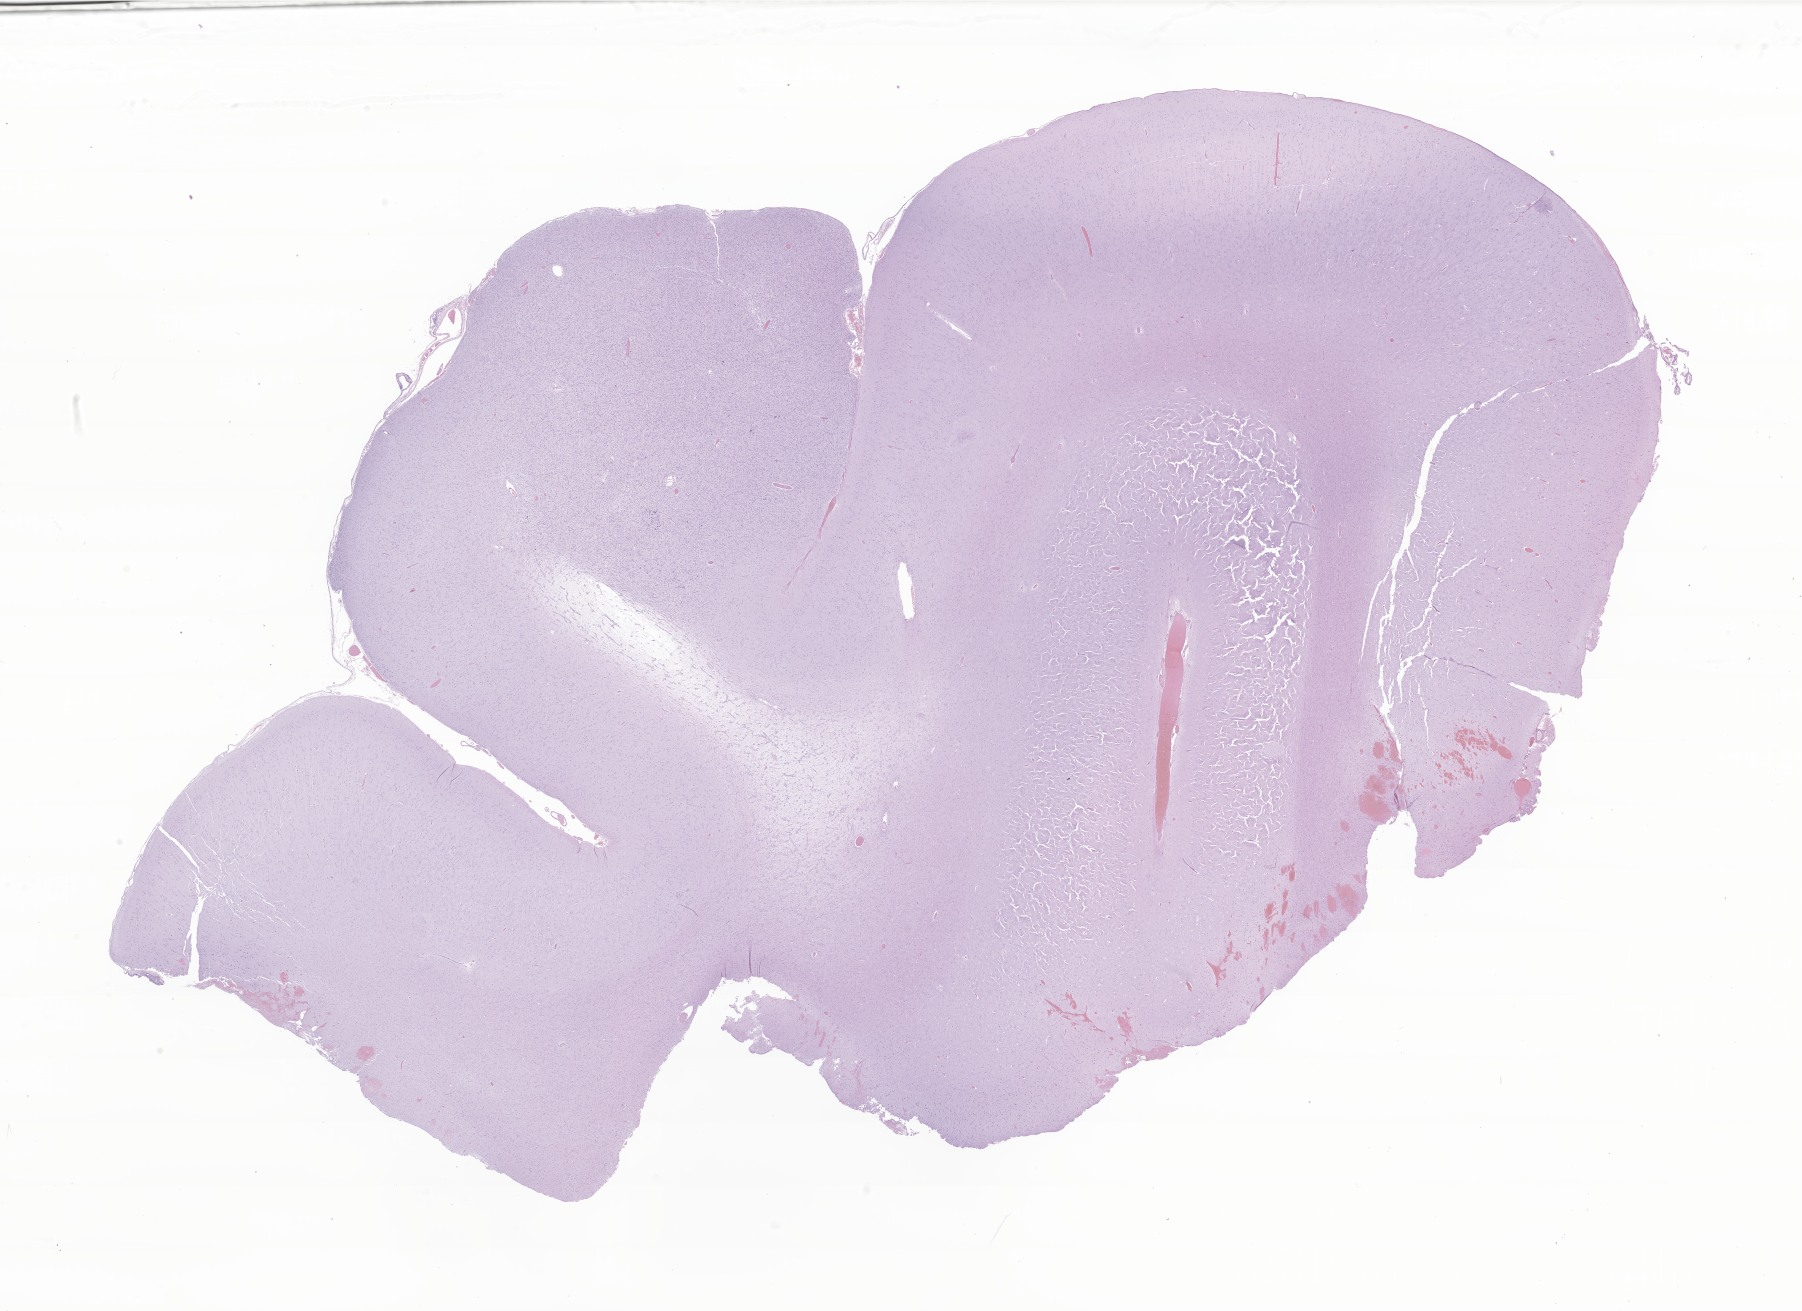
Whole-slide image, hematoxylin and eosin (H&E) stain of tumor tissue from the temporal lobe, whole scanned area (about 30.4 x 22.1 mm) shown as a low-resolution overview. Formalin-fixed, paraffin-embedded (FFPE) tissue. Female patient, age 176 months (14 years 8 months).
Diagnosis: Ganglioglioma, NOS.